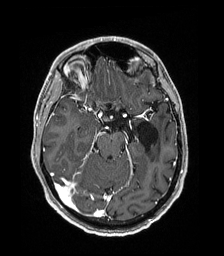
Brain MRI from a brain-tumour surgery series, one axial slice. Slice 115 of 192 in the series (ordered by position). T1-weighted post-contrast. 1 mm slice thickness. 224 × 256 image matrix, field of view 224 × 256 mm. Case-level facts recorded for this patient, not image findings: histopathology: Low grade glioma; IDH mutation: no.
Annotated regions visible in this slice (manually delineated by an expert):
- previous resection cavity: bounding box <136,121,158,153> (left, top, right, bottom; pixels)